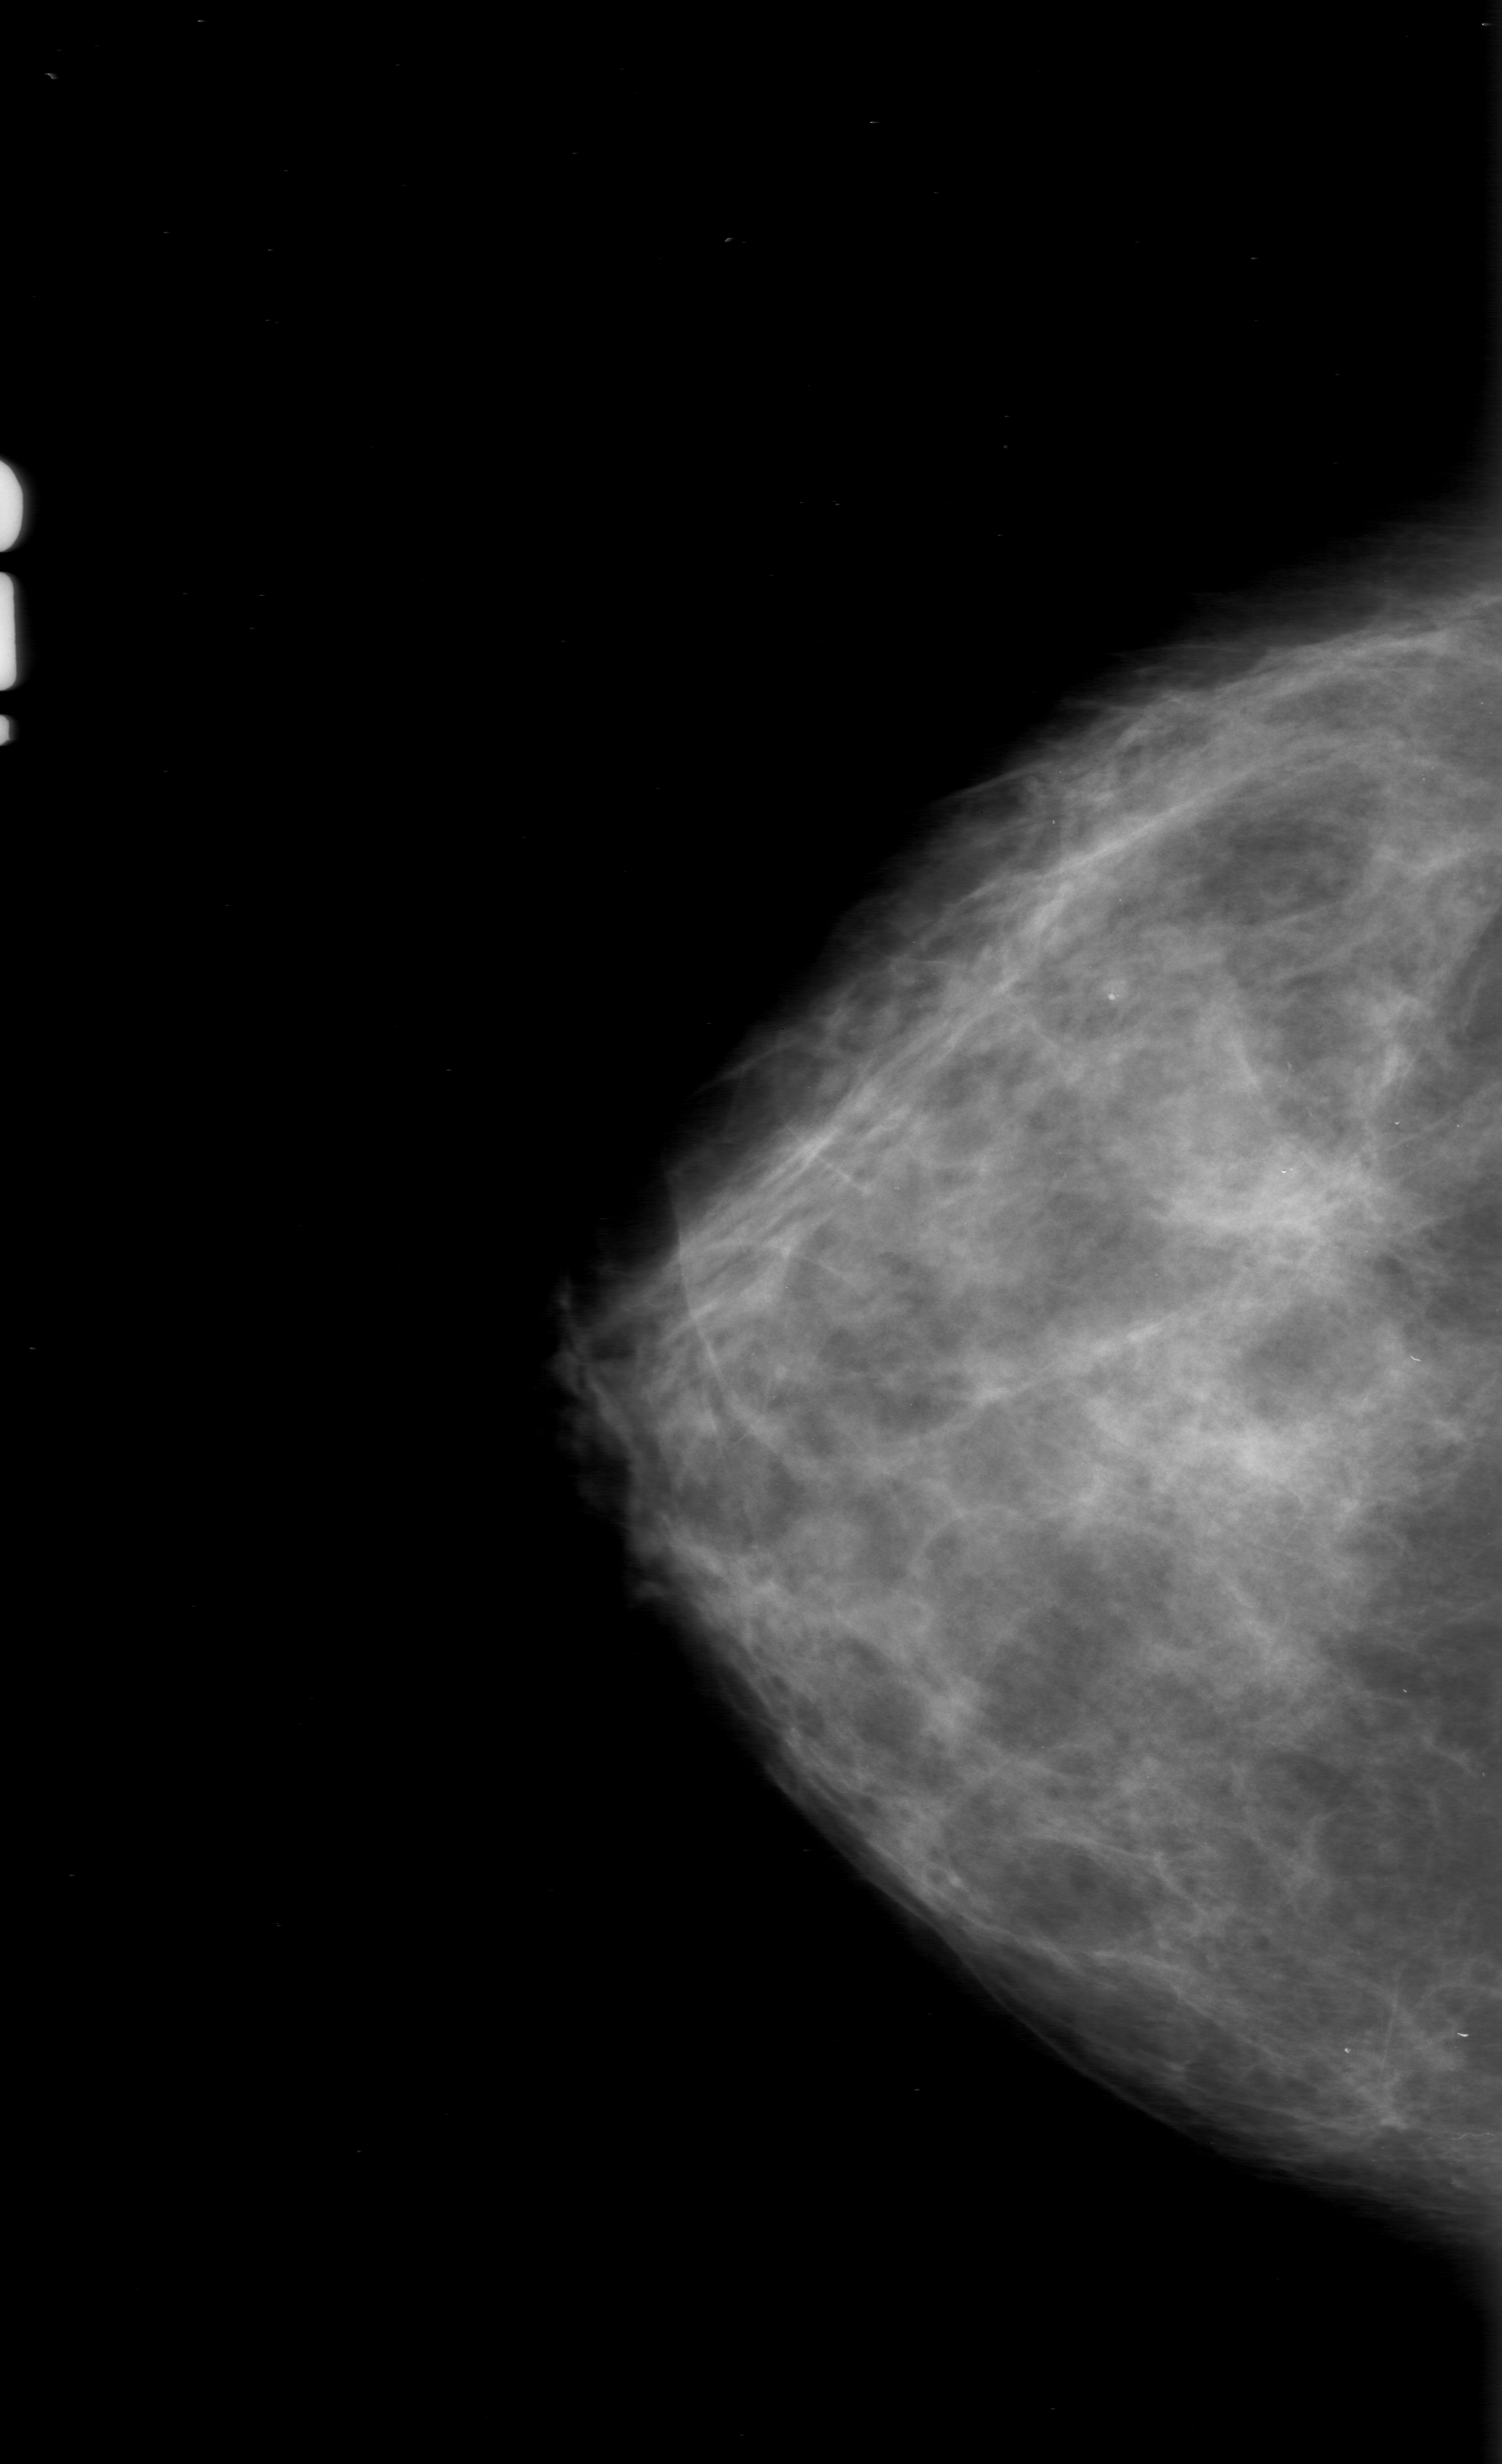
Scanned film-screen mammogram, right breast, craniocaudal (CC) view.
Calcifications, morphology punctate, distribution clustered; BI-RADS assessment category 0 (incomplete: needs additional imaging); subtlety rating 2 on a 1 (subtle) to 5 (obvious) scale; pathology (as recorded): malignant.